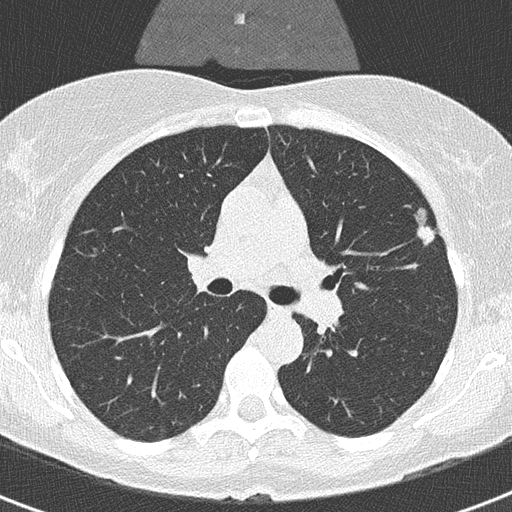
Low-dose screening chest CT, one axial slice. Slice 208 of 320 in the series (ordered by position). Reconstruction kernel B50f. Lung window (W 1500 / L -600 HU). 2 mm slice thickness. 512 × 512 image matrix, field of view 290 × 290 mm.
Outlined on this slice (outlined manually by an expert reader):
- lesion 1 (tumor, upper lobe of left lung): bounding box [x1, y1, x2, y2] px = [416, 209, 434, 245]